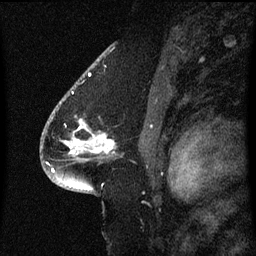
Breast MRI (dynamic contrast-enhanced), one sagittal slice. Position 40 of 60 along the scan axis. Dynamic contrast-enhanced series, image 2 of 3 at this slice position (ordered by acquisition). 1.5 T. TE 4.2 ms, TR 8.4 ms. 2 mm slice thickness. 256 × 256 image matrix, field of view 200 × 200 mm. Patient: female, 54 years. Case-level facts recorded for this patient, not image findings: setting: breast cancer imaged before/during neoadjuvant chemotherapy; receptor status: HR-positive, HER2-negative.
Outlined on this slice (semi-automatically segmented with operator editing):
- analysis volume of interest (the breast-tissue region the enhancement analysis was run in; not a lesion): bounding box [x1, y1, x2, y2] px = [49, 102, 114, 161]
- tumour enhancement mask (voxels above the 70 % enhancement threshold inside the analysis volume of interest): [65, 136, 113, 155]